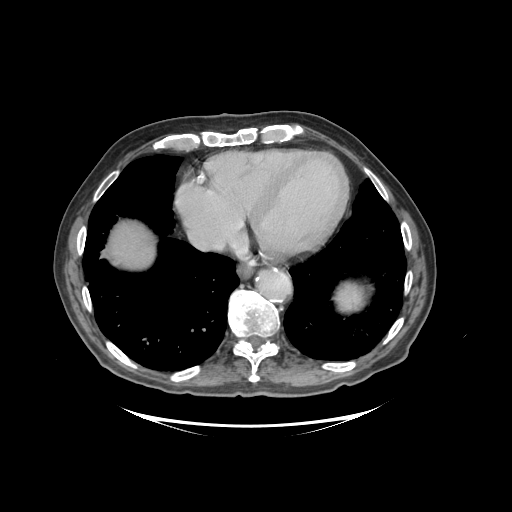
Contrast-enhanced abdominal CT (liver protocol), one axial slice. Slice 91 of 99 in the series (ordered by position). 140 kVp. Soft-tissue window (W 400 / L 40 HU). 512 × 512 image matrix. From the clinical record (not read from this slice): diagnosis: hepatocellular carcinoma (patient treated with transarterial chemoembolisation; whether this scan precedes or follows treatment is not stated here); TNM stage (as recorded): Stage-I.
Structures marked on this image (semi-automatically segmented with operator editing):
- liver parenchyma outside the tumour (the mass and vessels are separate outlines, so this box may not span the whole liver): bounding box [x1, y1, x2, y2] px = [107, 222, 154, 268]